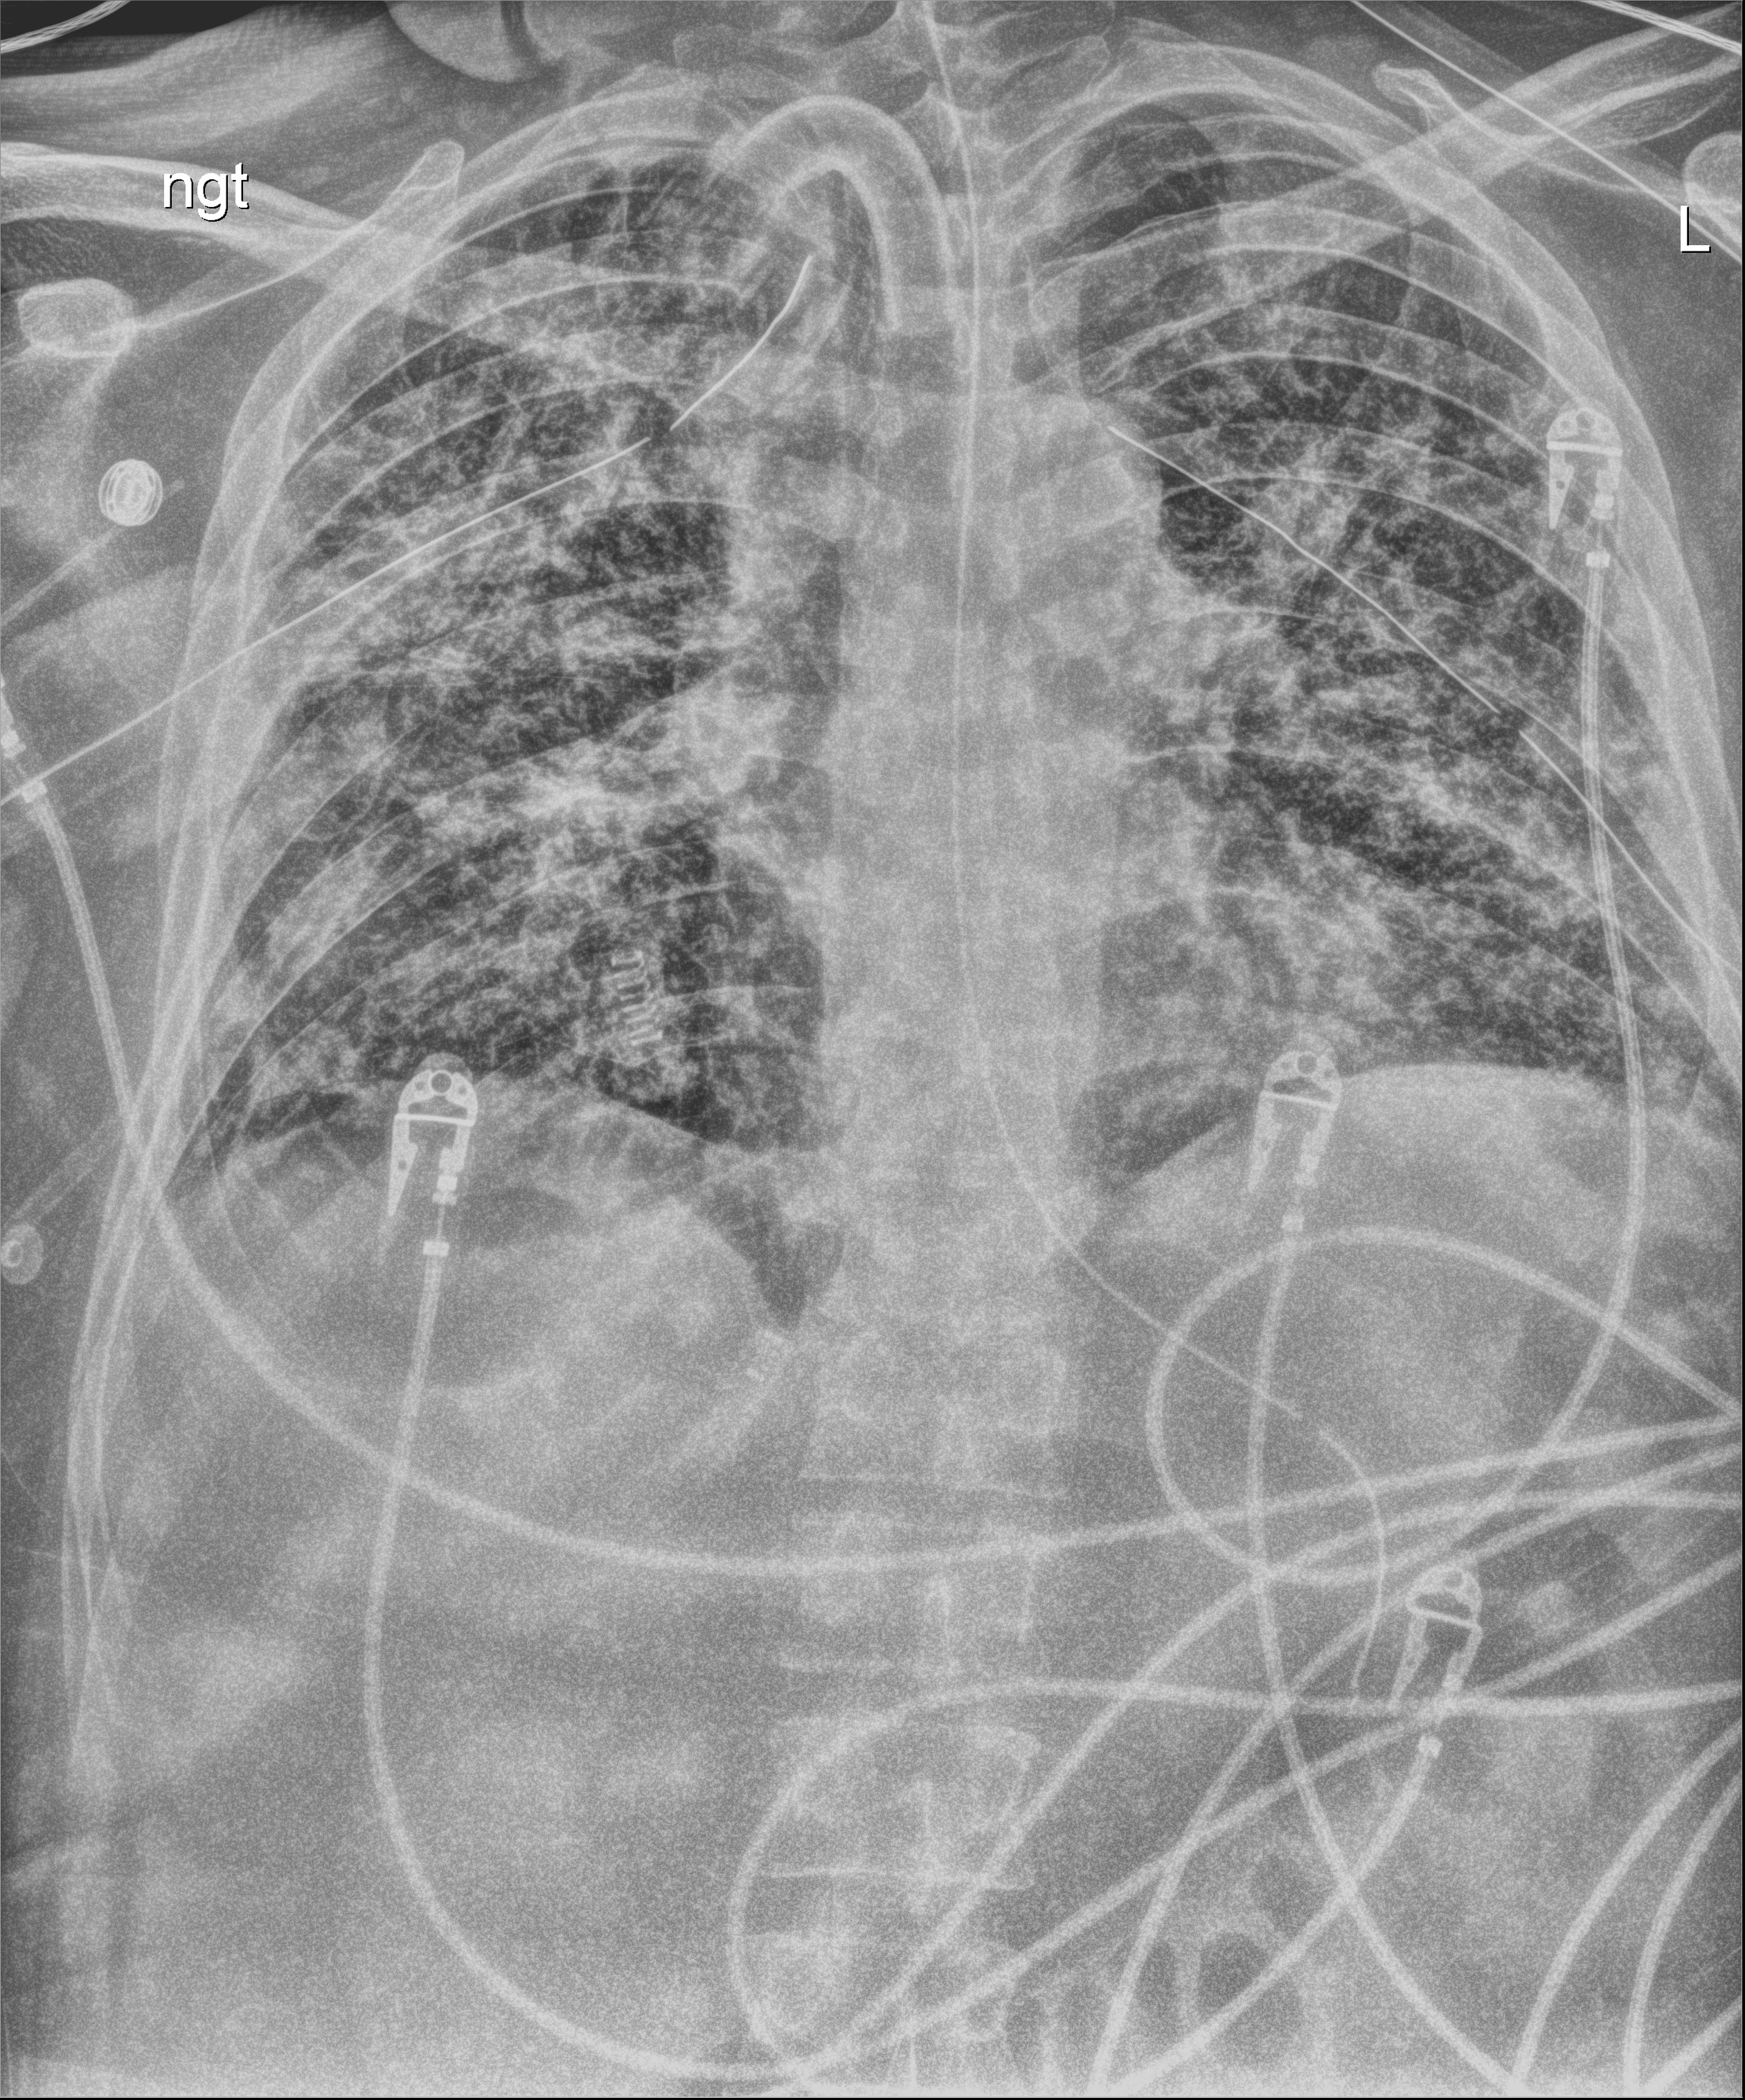
Chest X-ray (portable), anteroposterior (AP) projection. Male patient hospitalised with COVID-19, age 18–59 years.
From the hospital-stay record, not from the radiograph (when in the stay this image was taken is not recorded):
- smoking status (admission record): never
- hypertension (admission record): yes